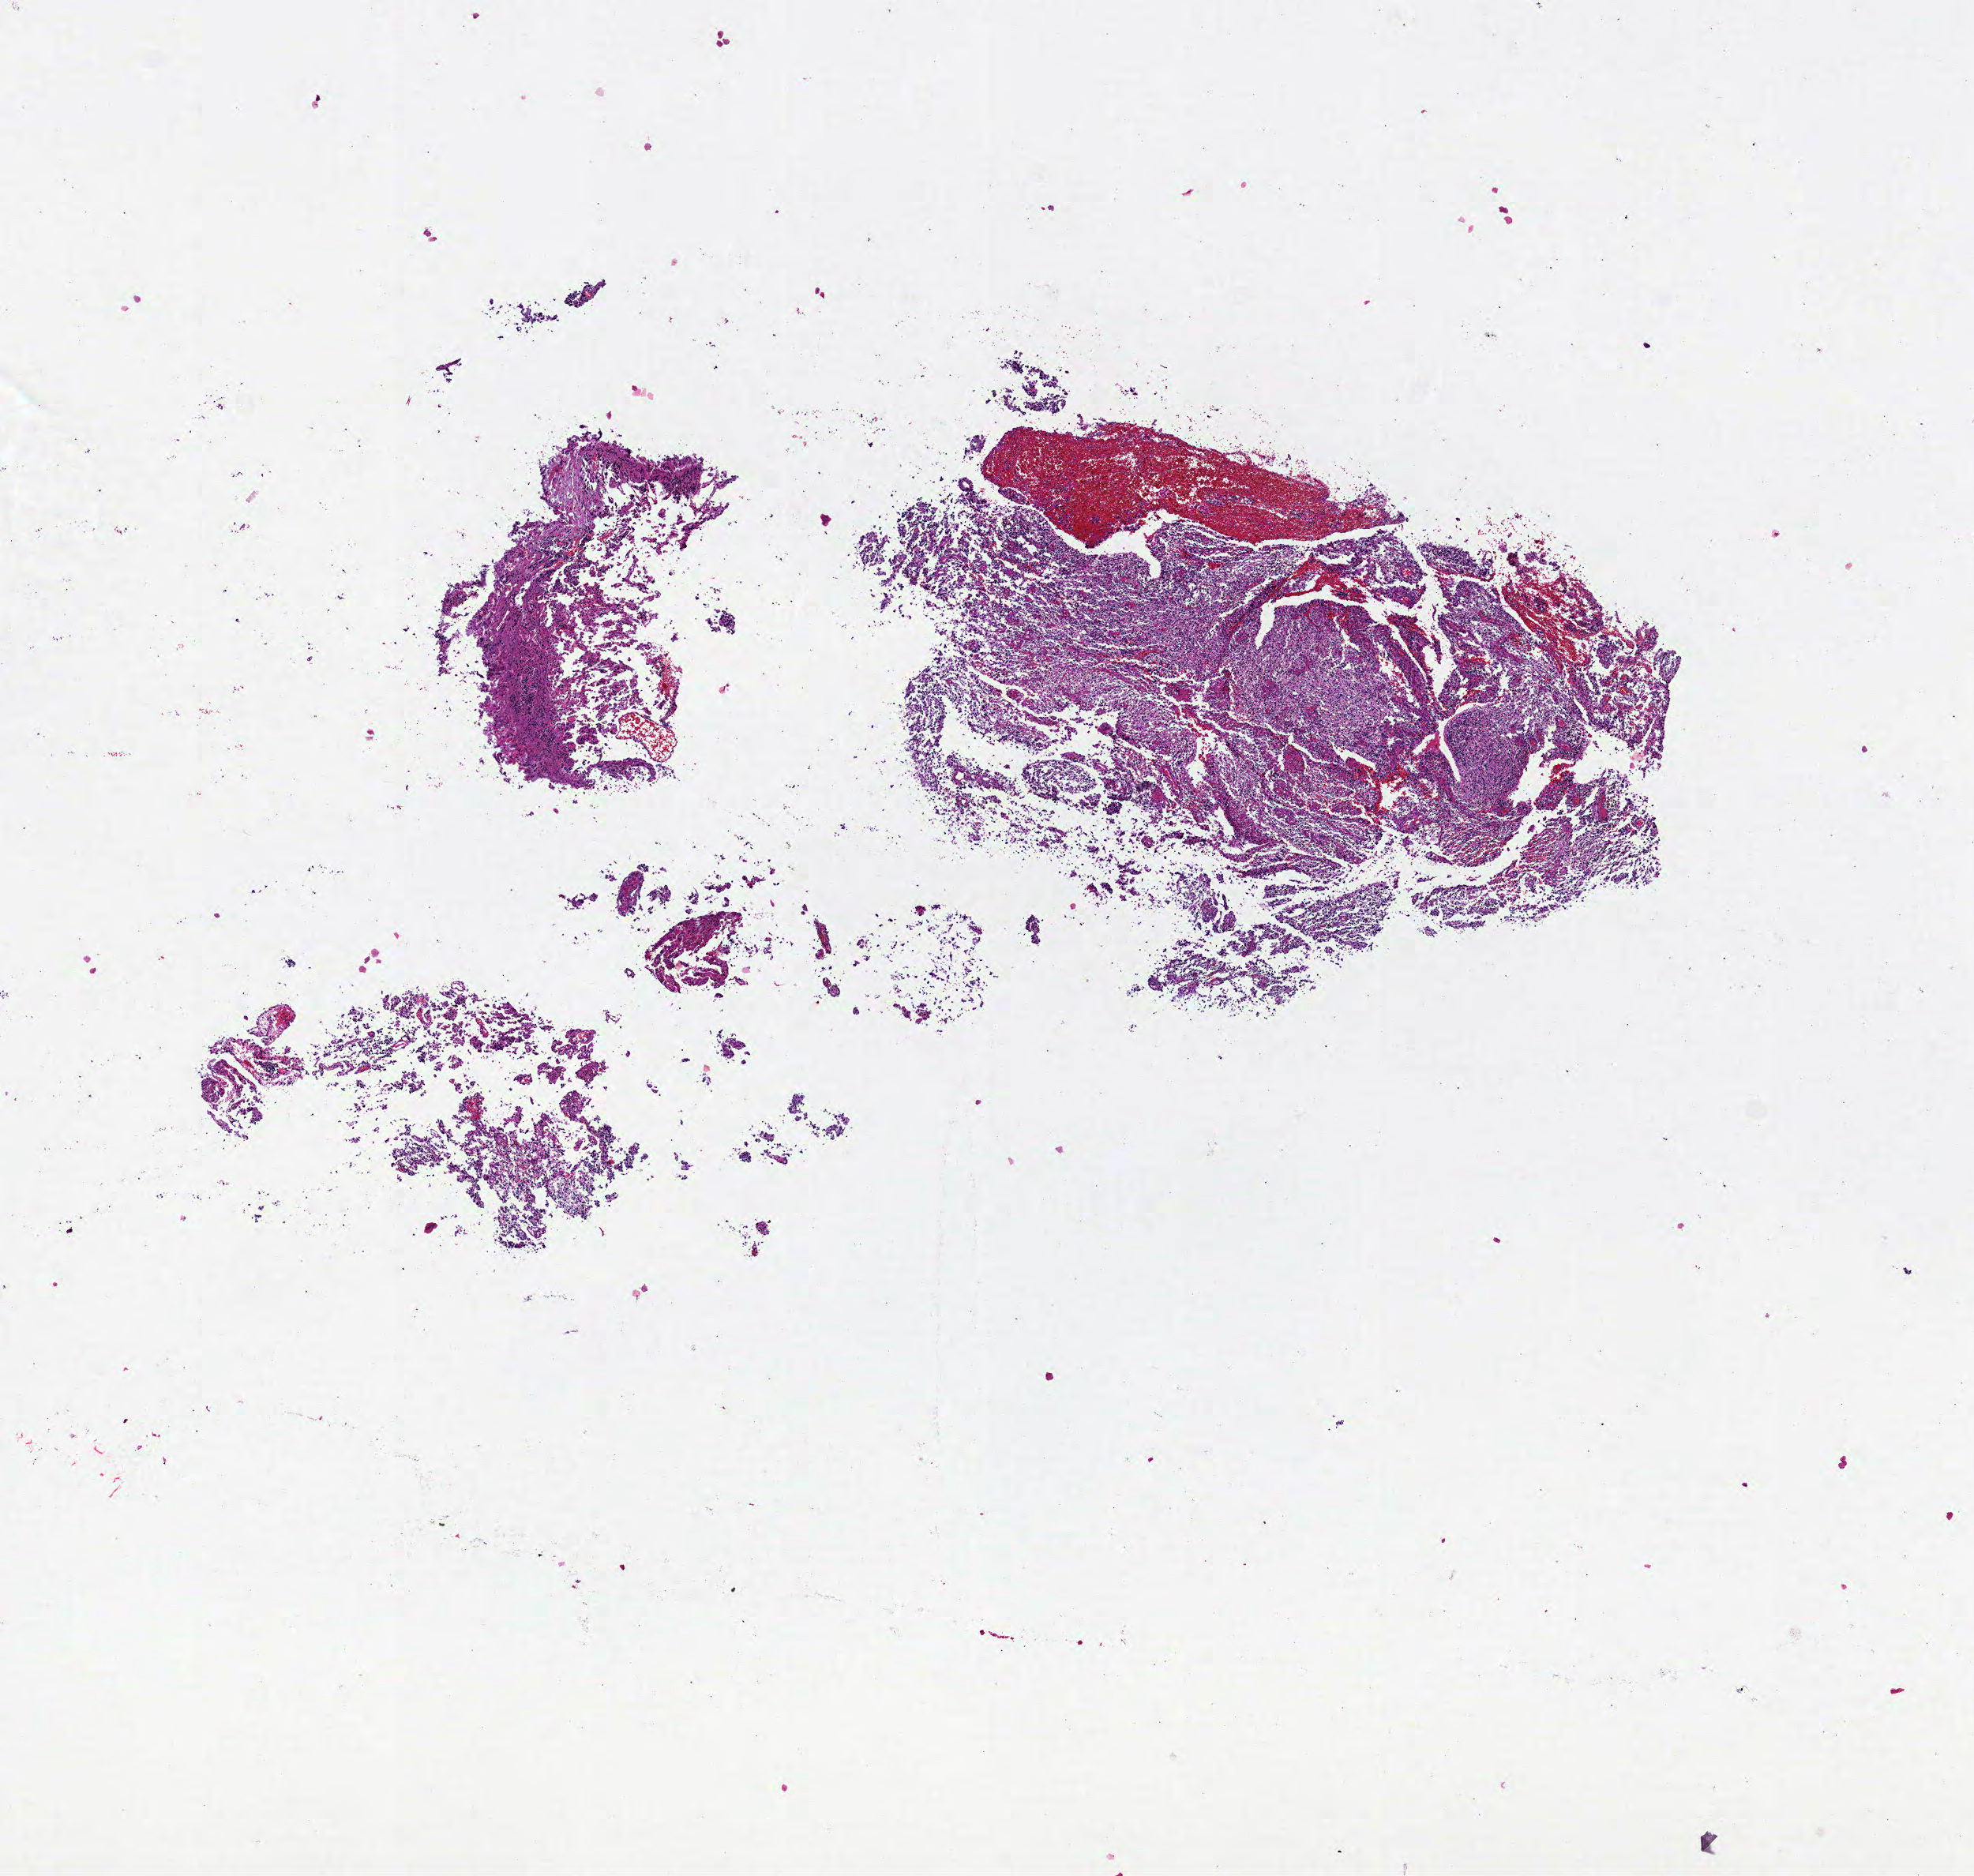
Whole-slide histology image, H&E, whole scanned area (about 10.0 x 9.5 mm) shown as a low-resolution overview, formalin-fixed paraffin-embedded (FFPE) diagnostic section, brain, primary tumour sample. Patient: male, age at initial diagnosis 40 years.
* histologic diagnosis: Glioblastoma